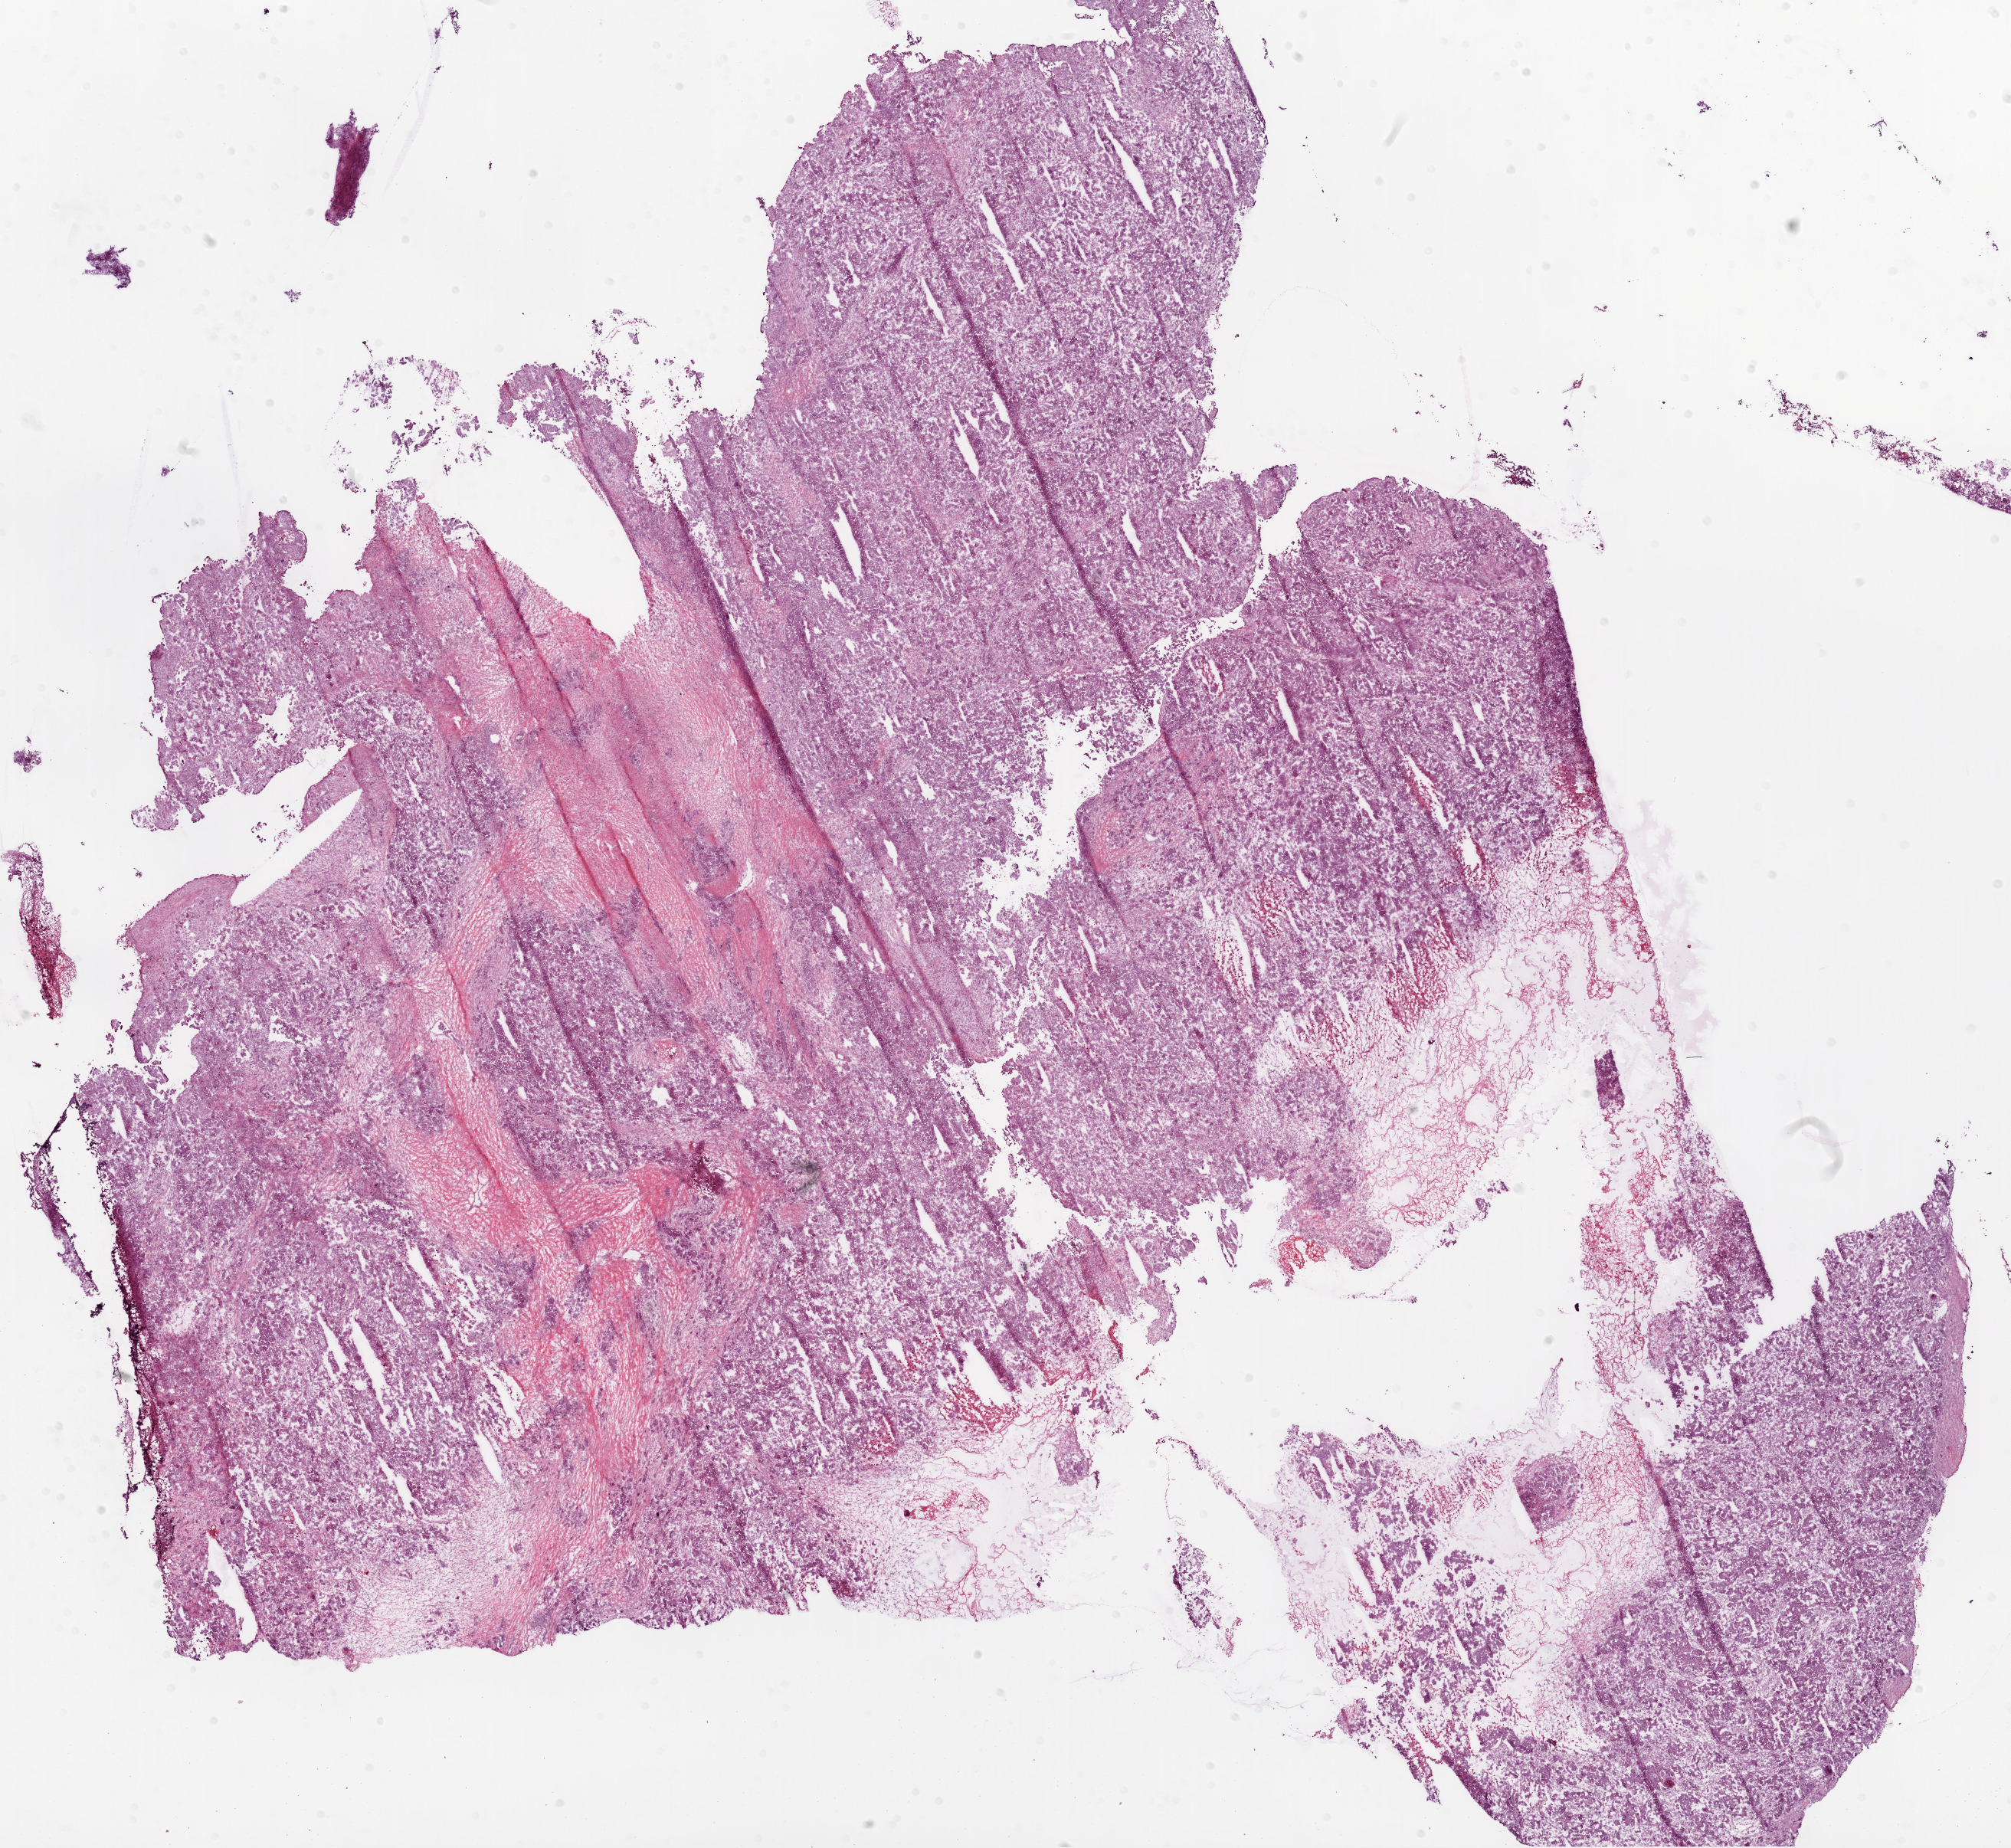
H&E whole-slide image — shown as a low-resolution overview of the whole scanned area (about 21.1 x 19.4 mm); frozen section; primary tumour sample from the ovary. Patient: female, age at initial diagnosis 65 years. Histologic grade: G3 (poorly differentiated). Pathologist review of this section (percent, as recorded): tumour cells 85%, tumour nuclei 90%, normal cells 0%, stromal cells 10%, necrosis 5%.
* histologic diagnosis: Serous cystadenocarcinoma, NOS
* FIGO stage: IIIC